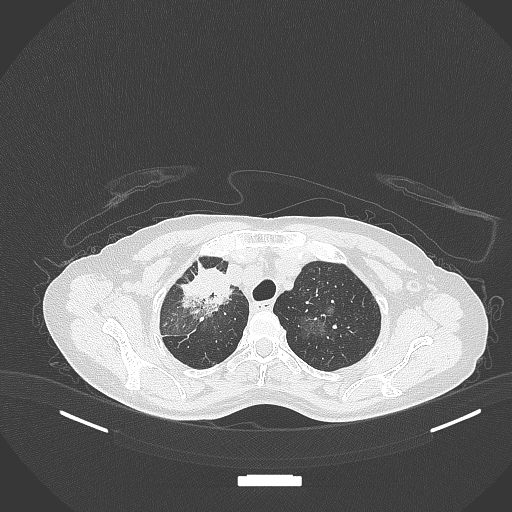
Chest CT, one axial slice. Slice 268 of 284 in the series (ordered by position). Reconstruction kernel B70f. Lung window (W 1500 / L -600 HU). 1 mm slice thickness. 512 × 512 image matrix. Patient: female, 59 years. From the clinical record (not read from this slice): clinical TNM (as recorded): T3 N0 M0; histopathological grade: G1.
Annotated regions visible in this slice (rectangle marked by the reading radiologist):
- lung tumour (recorded histology: adenocarcinoma): bounding box <174,263,230,320> (left, top, right, bottom; pixels)